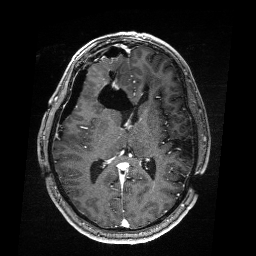
Brain MRI from a brain-tumour surgery series, one axial slice; slice 100 of 176 in the series (ordered by position); T1-weighted post-contrast; 256 × 256 image matrix, field of view 256 × 256 mm. Case-level facts recorded for this patient, not image findings: histopathology: Astrocytoma; WHO grade: 4; IDH mutation: yes; tumour location: Right Frontal.
Outlined on this slice (outlined manually by an expert reader):
- residual tumour: bounding box <112,82,117,136> (left, top, right, bottom; pixels)